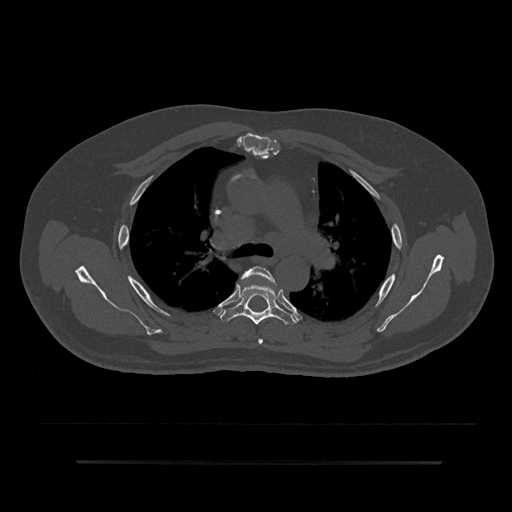
CT including the spine, one axial slice; slice 584 of 797 in the series (ordered by position); 120 kVp; bone window (W 1800 / L 400 HU); 0.5 mm slice thickness; 512 × 512 image matrix, field of view 464 × 464 mm. Patient: male, 59 years. Case-level facts recorded for this patient, not image findings: primary cancer: bile ducts; vertebrae with lytic lesions (as recorded): T10.
Outlined on this slice (semi-automatic segmentation, software-assisted and operator-edited):
- T4 vertebra: bounding box (x1, y1, x2, y2) in pixels: (241, 266, 277, 344)
- T5 vertebra: (220, 283, 297, 325)